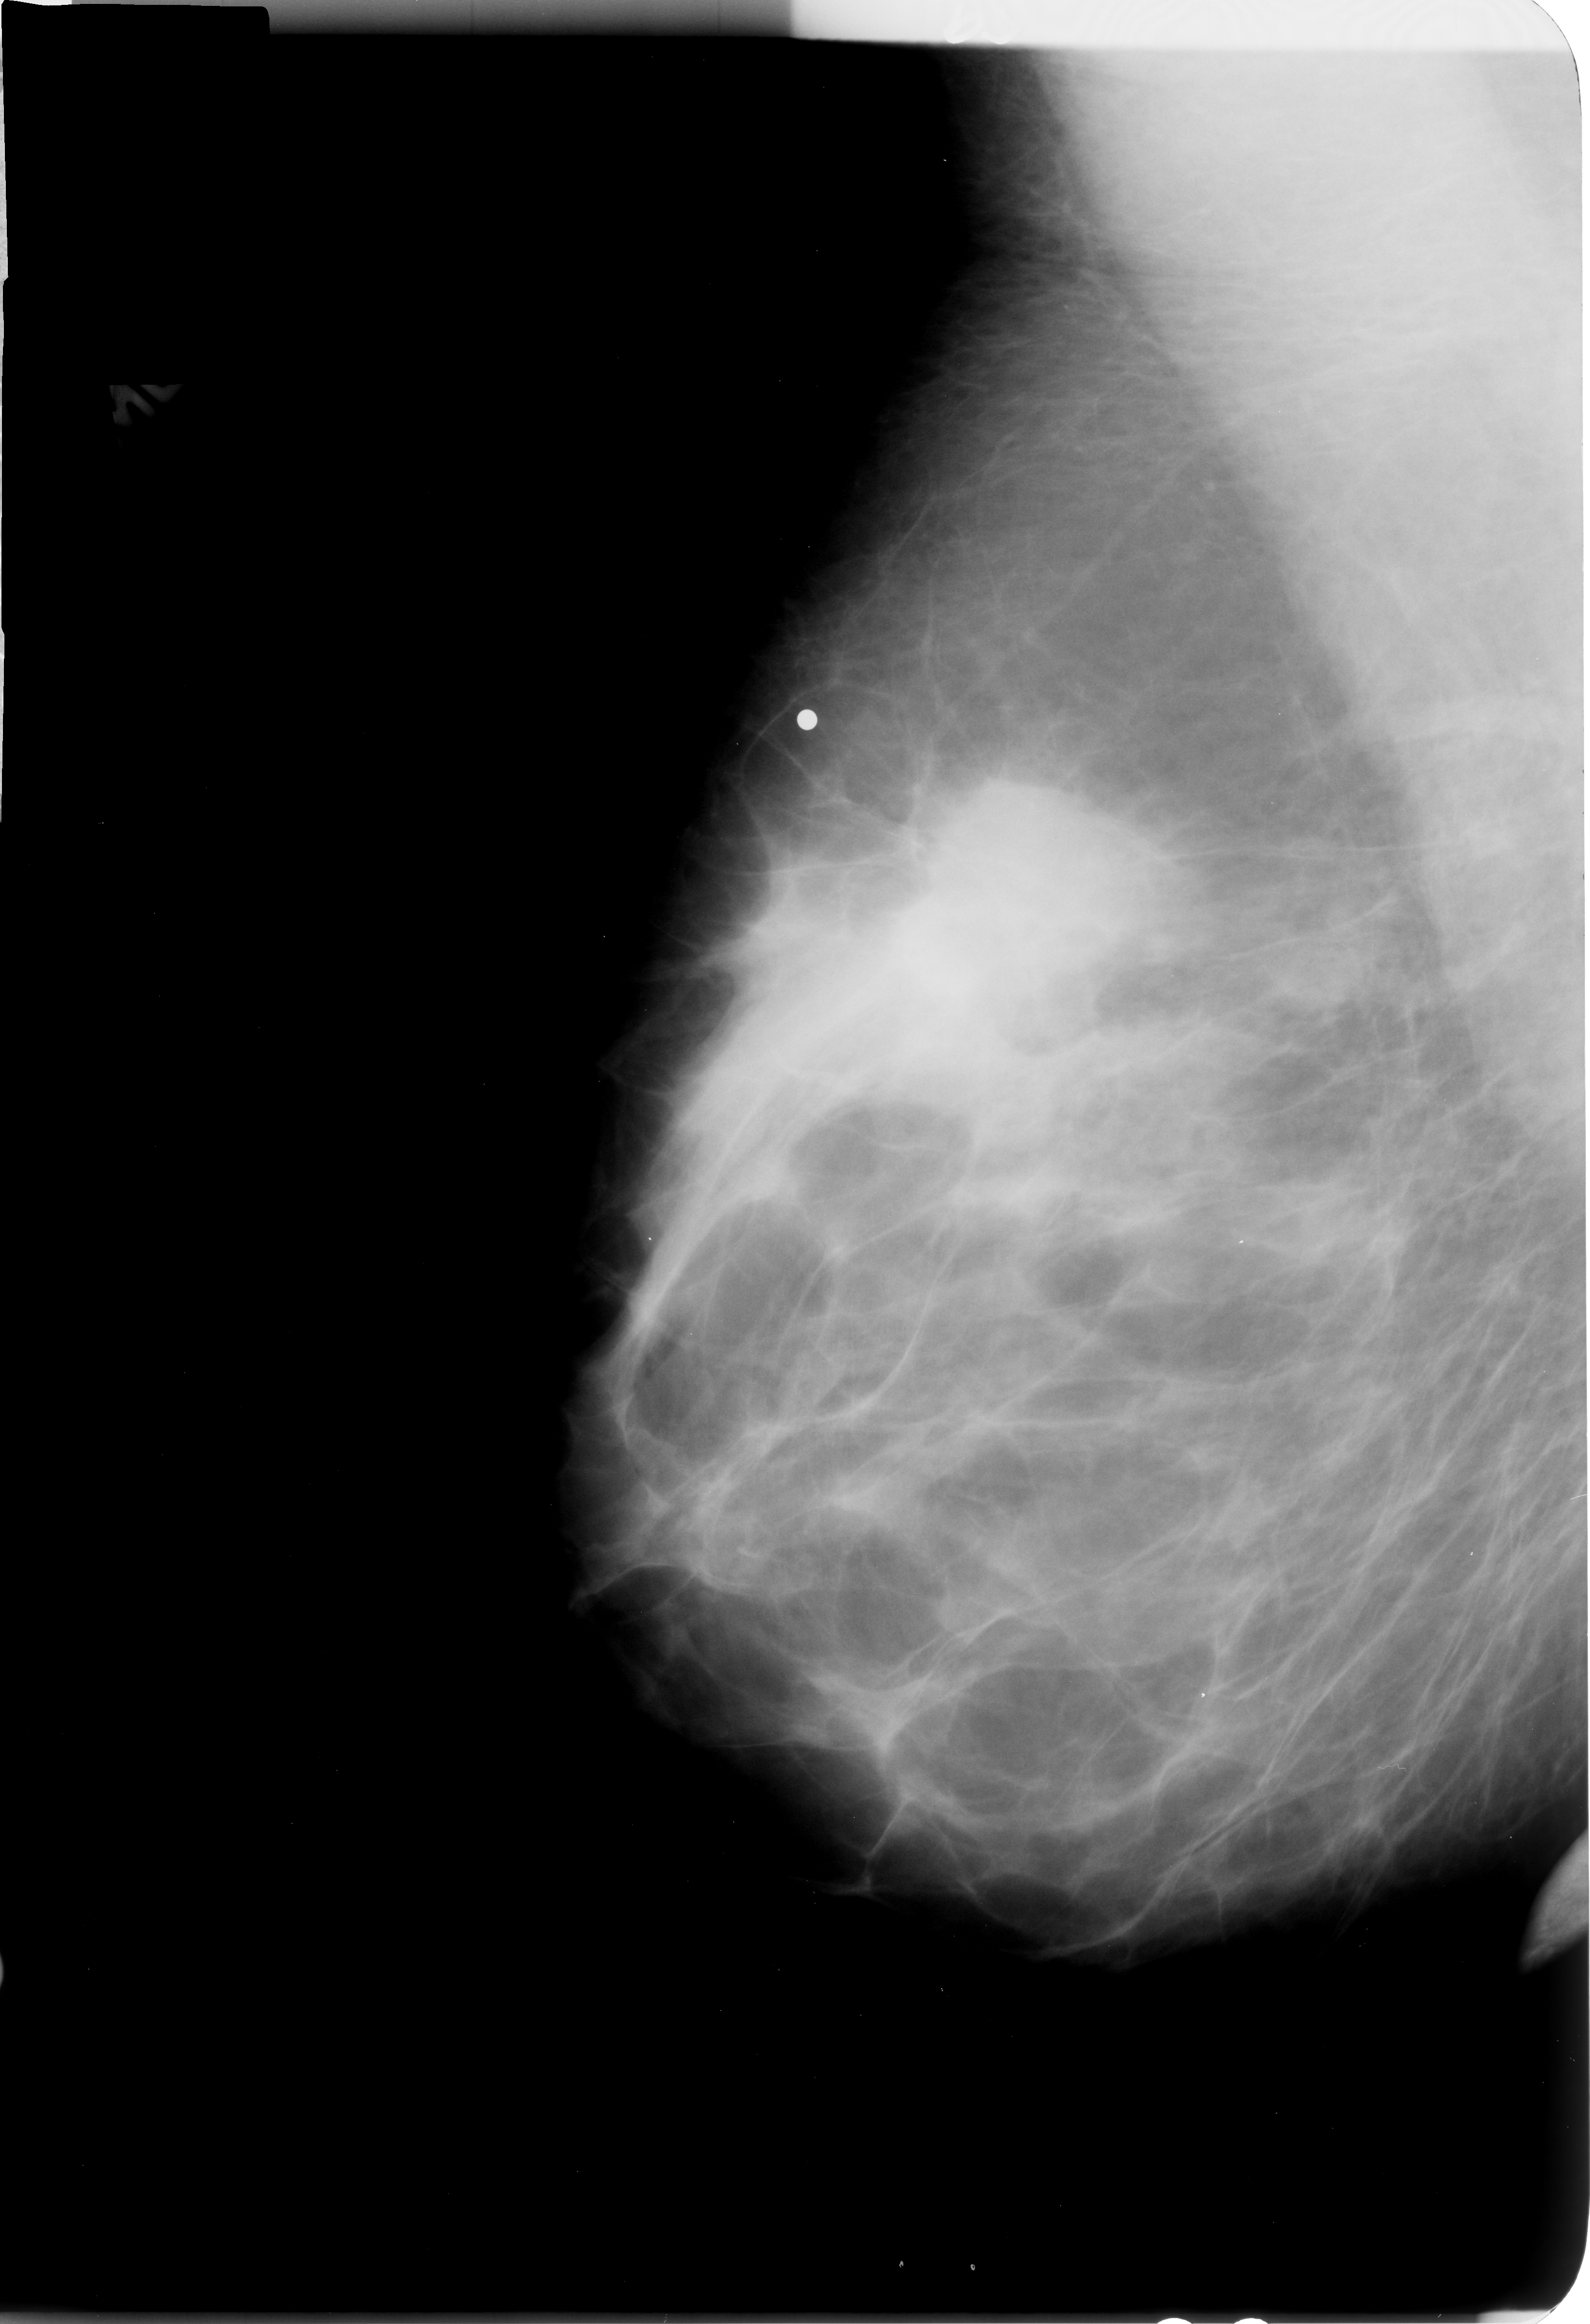
Mammogram (digitized film), right breast, MLO view, breast composition: heterogeneously dense (BI-RADS density category 3 of 4).
Abnormality record for this image: mass, shape irregular / architectural distortion, margins obscured / ill defined / spiculated; BI-RADS assessment category 4; pathology result (as recorded, not read from the image): malignant.